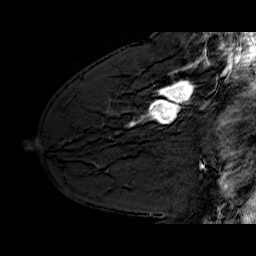
Breast MRI (dynamic contrast-enhanced), one sagittal slice; position 41 of 60 along the scan axis; dynamic contrast-enhanced series, time point 2 of 6 at this slice position (early post-contrast); 1.5 T; TE 6.4 ms, TR 32.9 ms; 4 mm slice thickness; 256 × 256 image matrix. Female patient. From the clinical record (not read from this slice): setting: breast cancer imaged before/during neoadjuvant chemotherapy; receptor status: HER2-positive.
Outlined on this slice (semi-automatically segmented with operator editing):
- analysis volume of interest (the breast-tissue region the enhancement analysis was run in; not a lesion): box from (x=130, y=62) to (x=210, y=128) px
- tumour enhancement mask (voxels above the 100 % enhancement threshold inside the analysis volume of interest): (x=130, y=62)–(x=199, y=126)